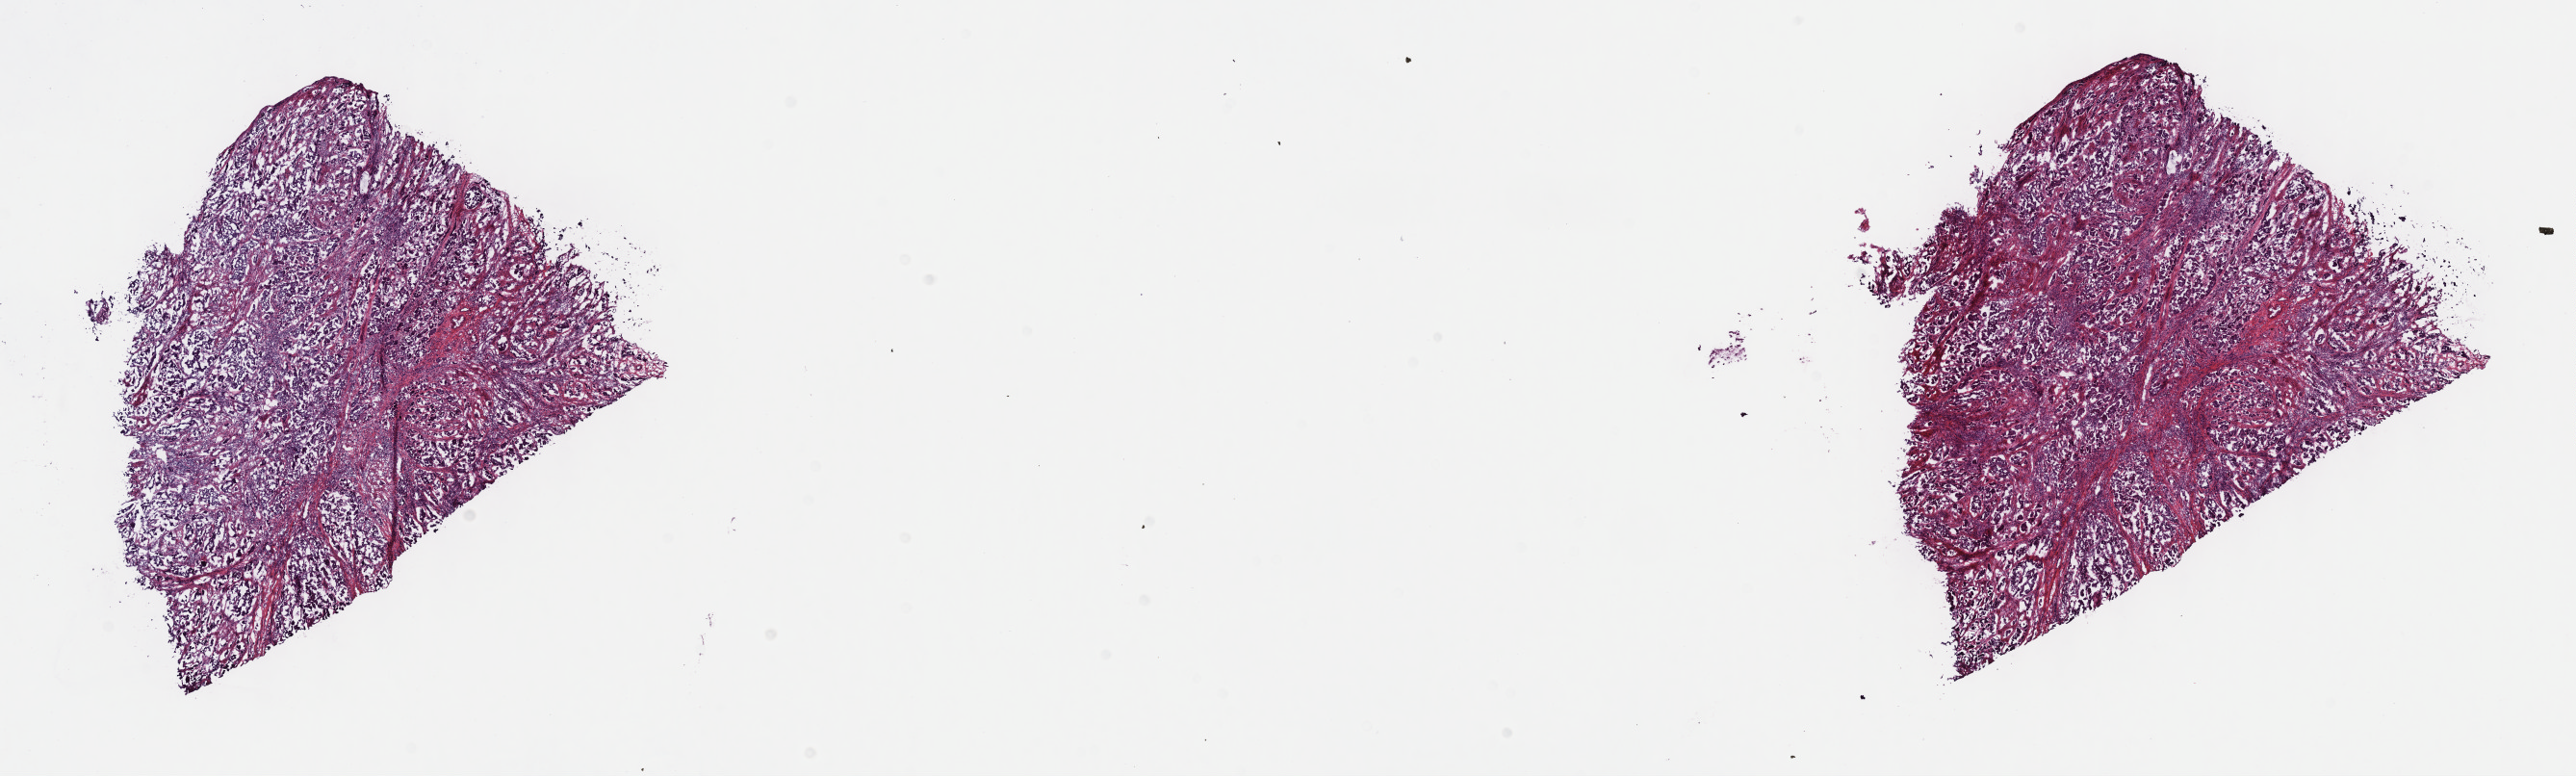
Digitized H&E tissue section (whole slide) — a low-resolution overview of the entire scanned area, about 21.6 x 6.5 mm (slide scanned at 40x), frozen section from the top of the tissue portion, primary tumour sample from the bladder. Male, age 75 years at initial diagnosis. Histologic grade: high grade. Composition of this section per pathologist review: tumour cells 75%, tumour nuclei 75%, normal cells 0%, stromal cells 25%, necrosis 0%. Inflammatory infiltration, as recorded: lymphocyte infiltration 3%, monocyte infiltration 2%, neutrophil infiltration 5%.
Diagnosis: Transitional cell carcinoma. TNM: T4a N2 MX. AJCC pathologic stage: IV (7th edition).